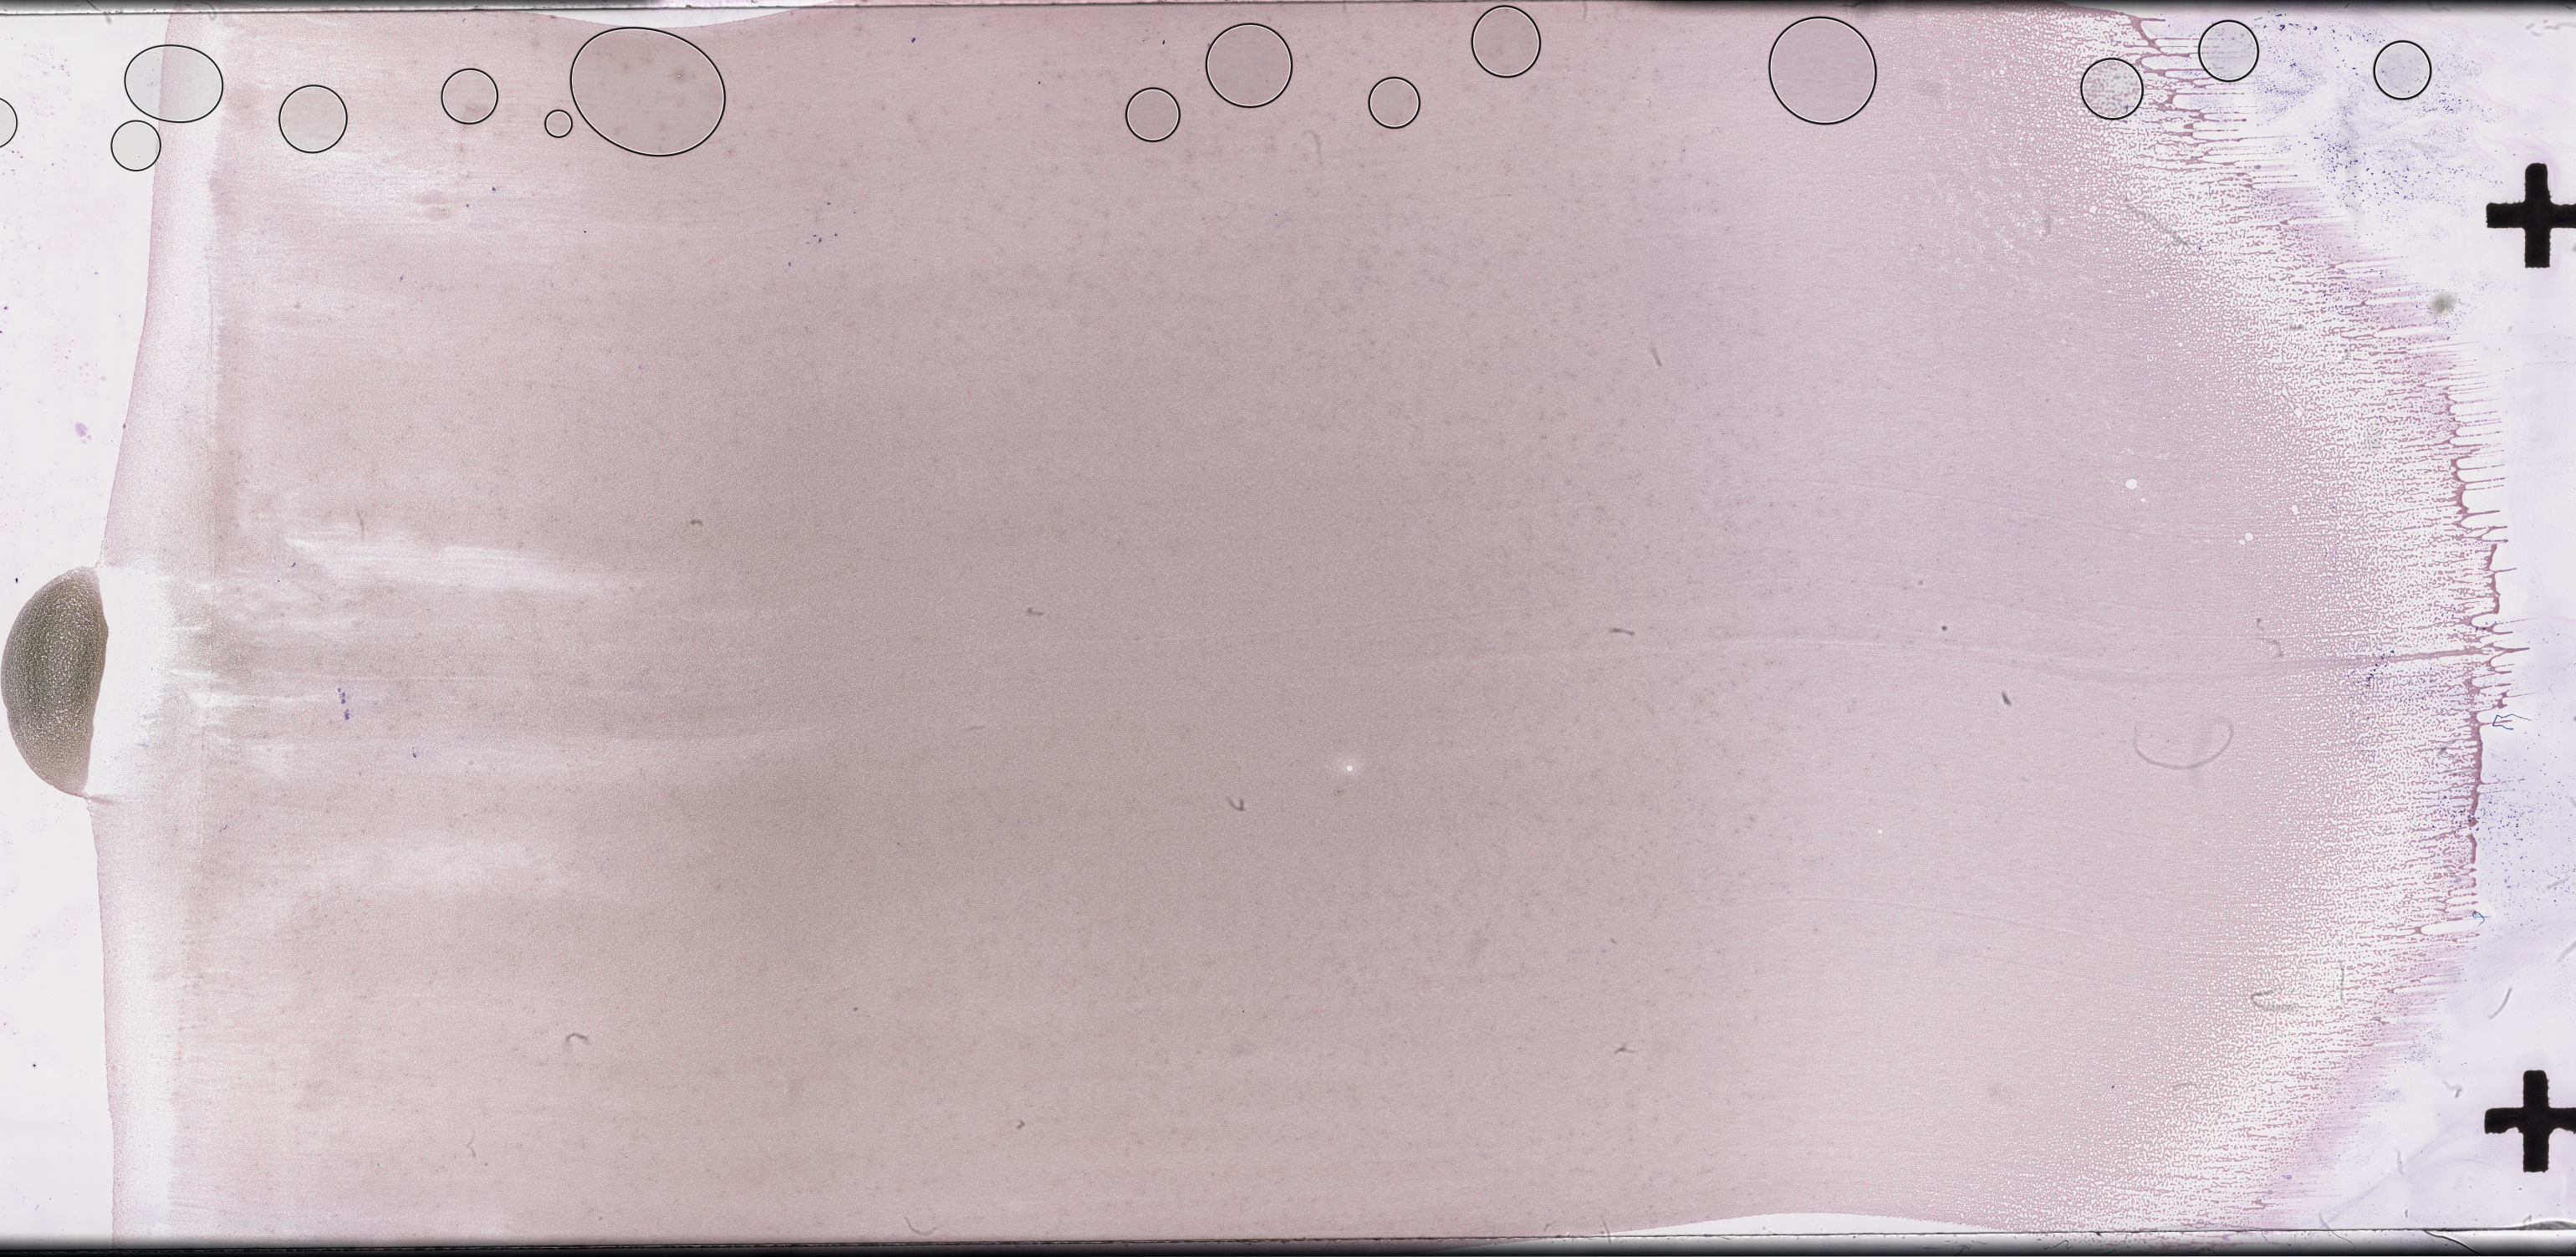
Whole-slide image of a whole blood smear, Wright–Giemsa stain — low-resolution overview of the scanned area, about 49.8 x 24.3 mm. Collected on treatment. Patient sex: male.
From a patient with: Plasma Cell Myeloma.